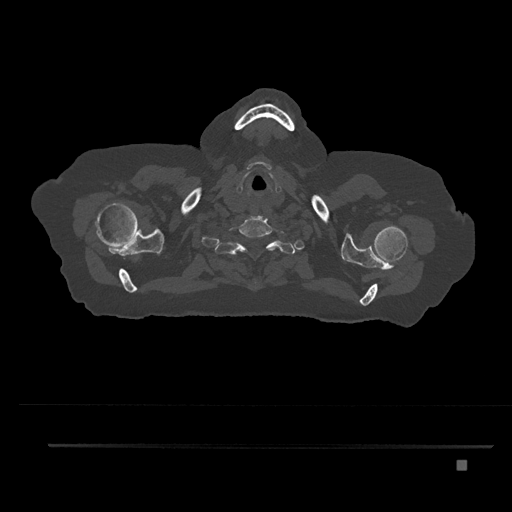
CT including the spine, one axial slice. Position 711 of 797 along the scan axis. Bone window (W 1800 / L 400 HU). 0.5 mm slice thickness. 512 × 512 image matrix. Female patient, age 76 years. From the clinical record (not read from this slice): primary cancer: lung; vertebrae with lytic lesions (as recorded): T11, L3.
Structures marked on this image (semi-automatic segmentation, software-assisted and operator-edited):
- T1 vertebra: bounding box (x1, y1, x2, y2) in pixels: (222, 237, 285, 257)